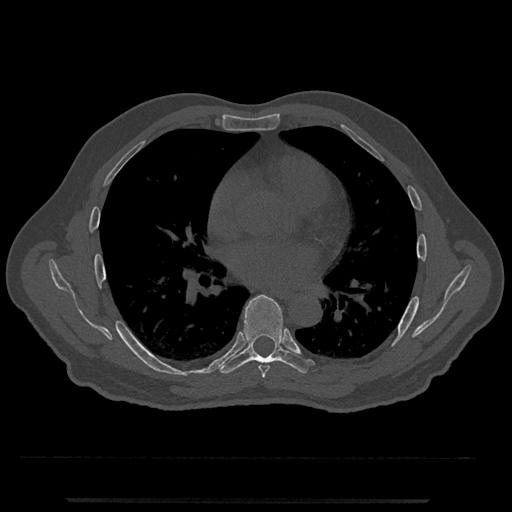
CT including the spine, one axial slice; slice 701 of 797 in the series (ordered by position); reconstruction kernel Br40s/3; 120 kVp; bone window (W 1800 / L 400 HU); 512 × 512 image matrix, field of view 419 × 419 mm. Patient: male, 63 years. Case-level facts recorded for this patient, not image findings: primary cancer: prostate.
Outlined on this slice (semi-automatic segmentation, software-assisted and operator-edited):
- T6 vertebra: bounding box <258,365,270,379> (left, top, right, bottom; pixels)
- T7 vertebra: <218,295,313,374>